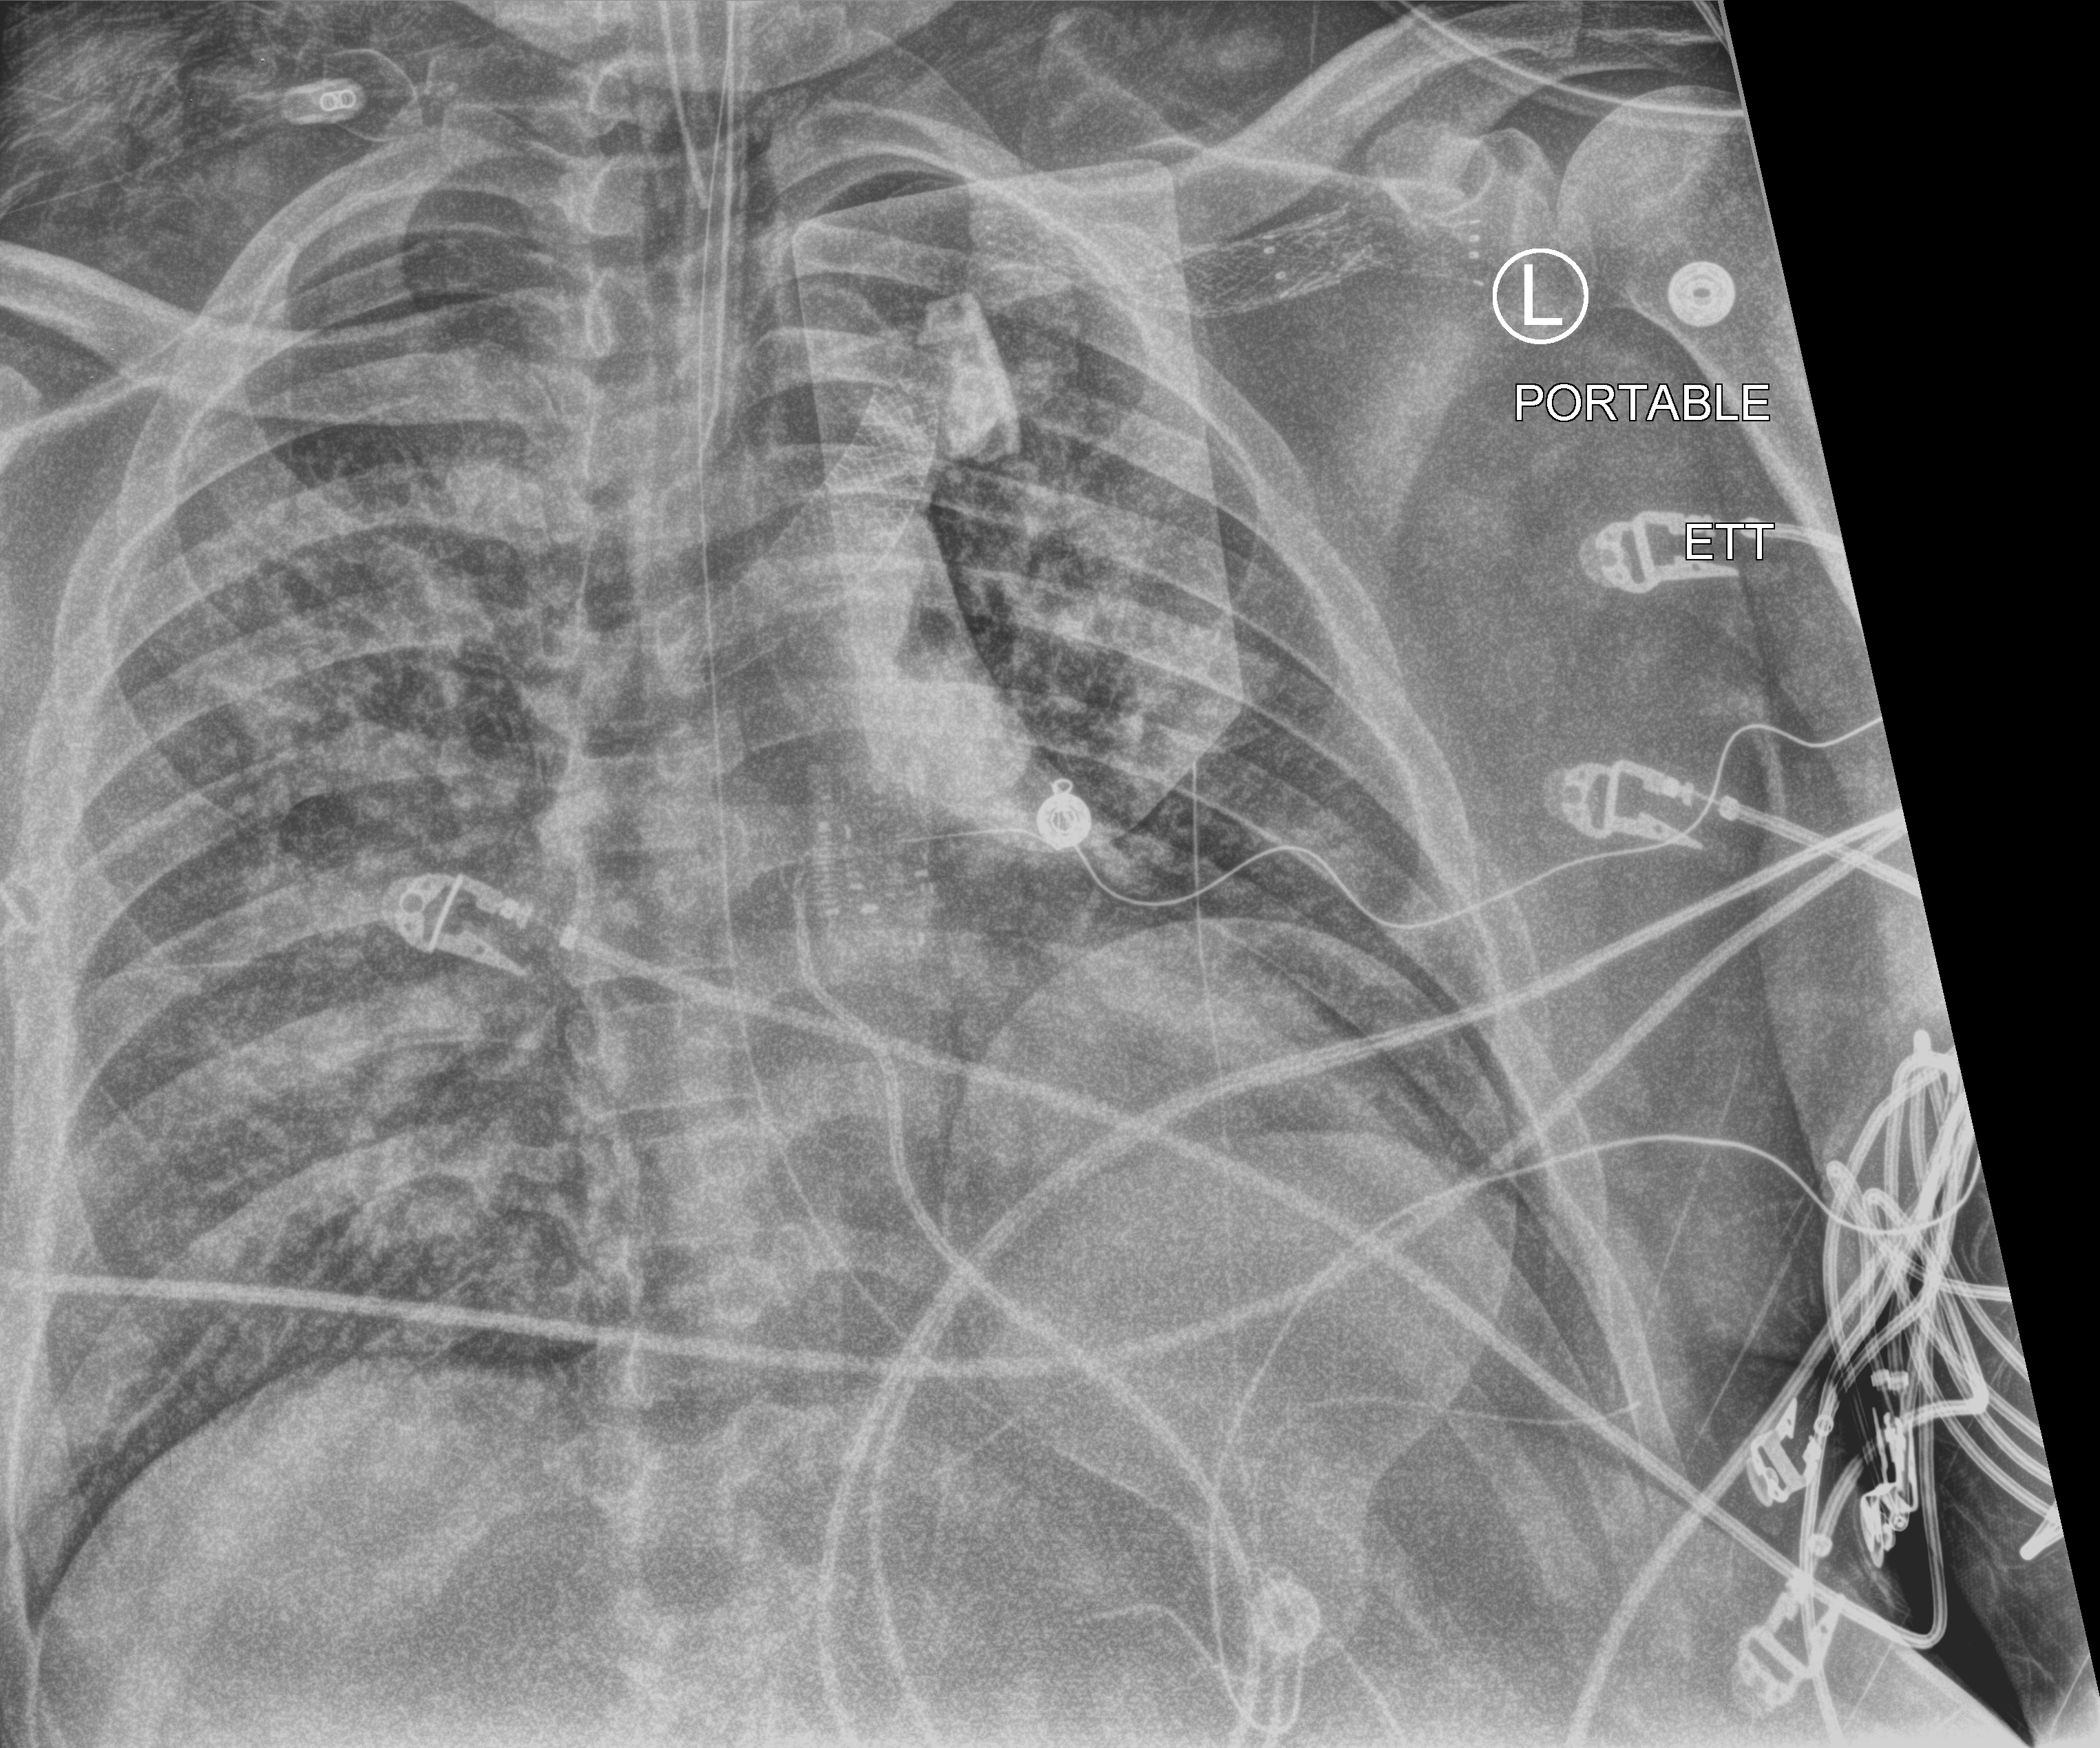
Portable chest radiograph, anteroposterior (AP) projection. Male patient hospitalised with COVID-19, age 18–59 years.
Hospital-stay facts (about this admission, not read from this image; timing relative to this image not recorded): mechanically ventilated during this hospital stay: yes.